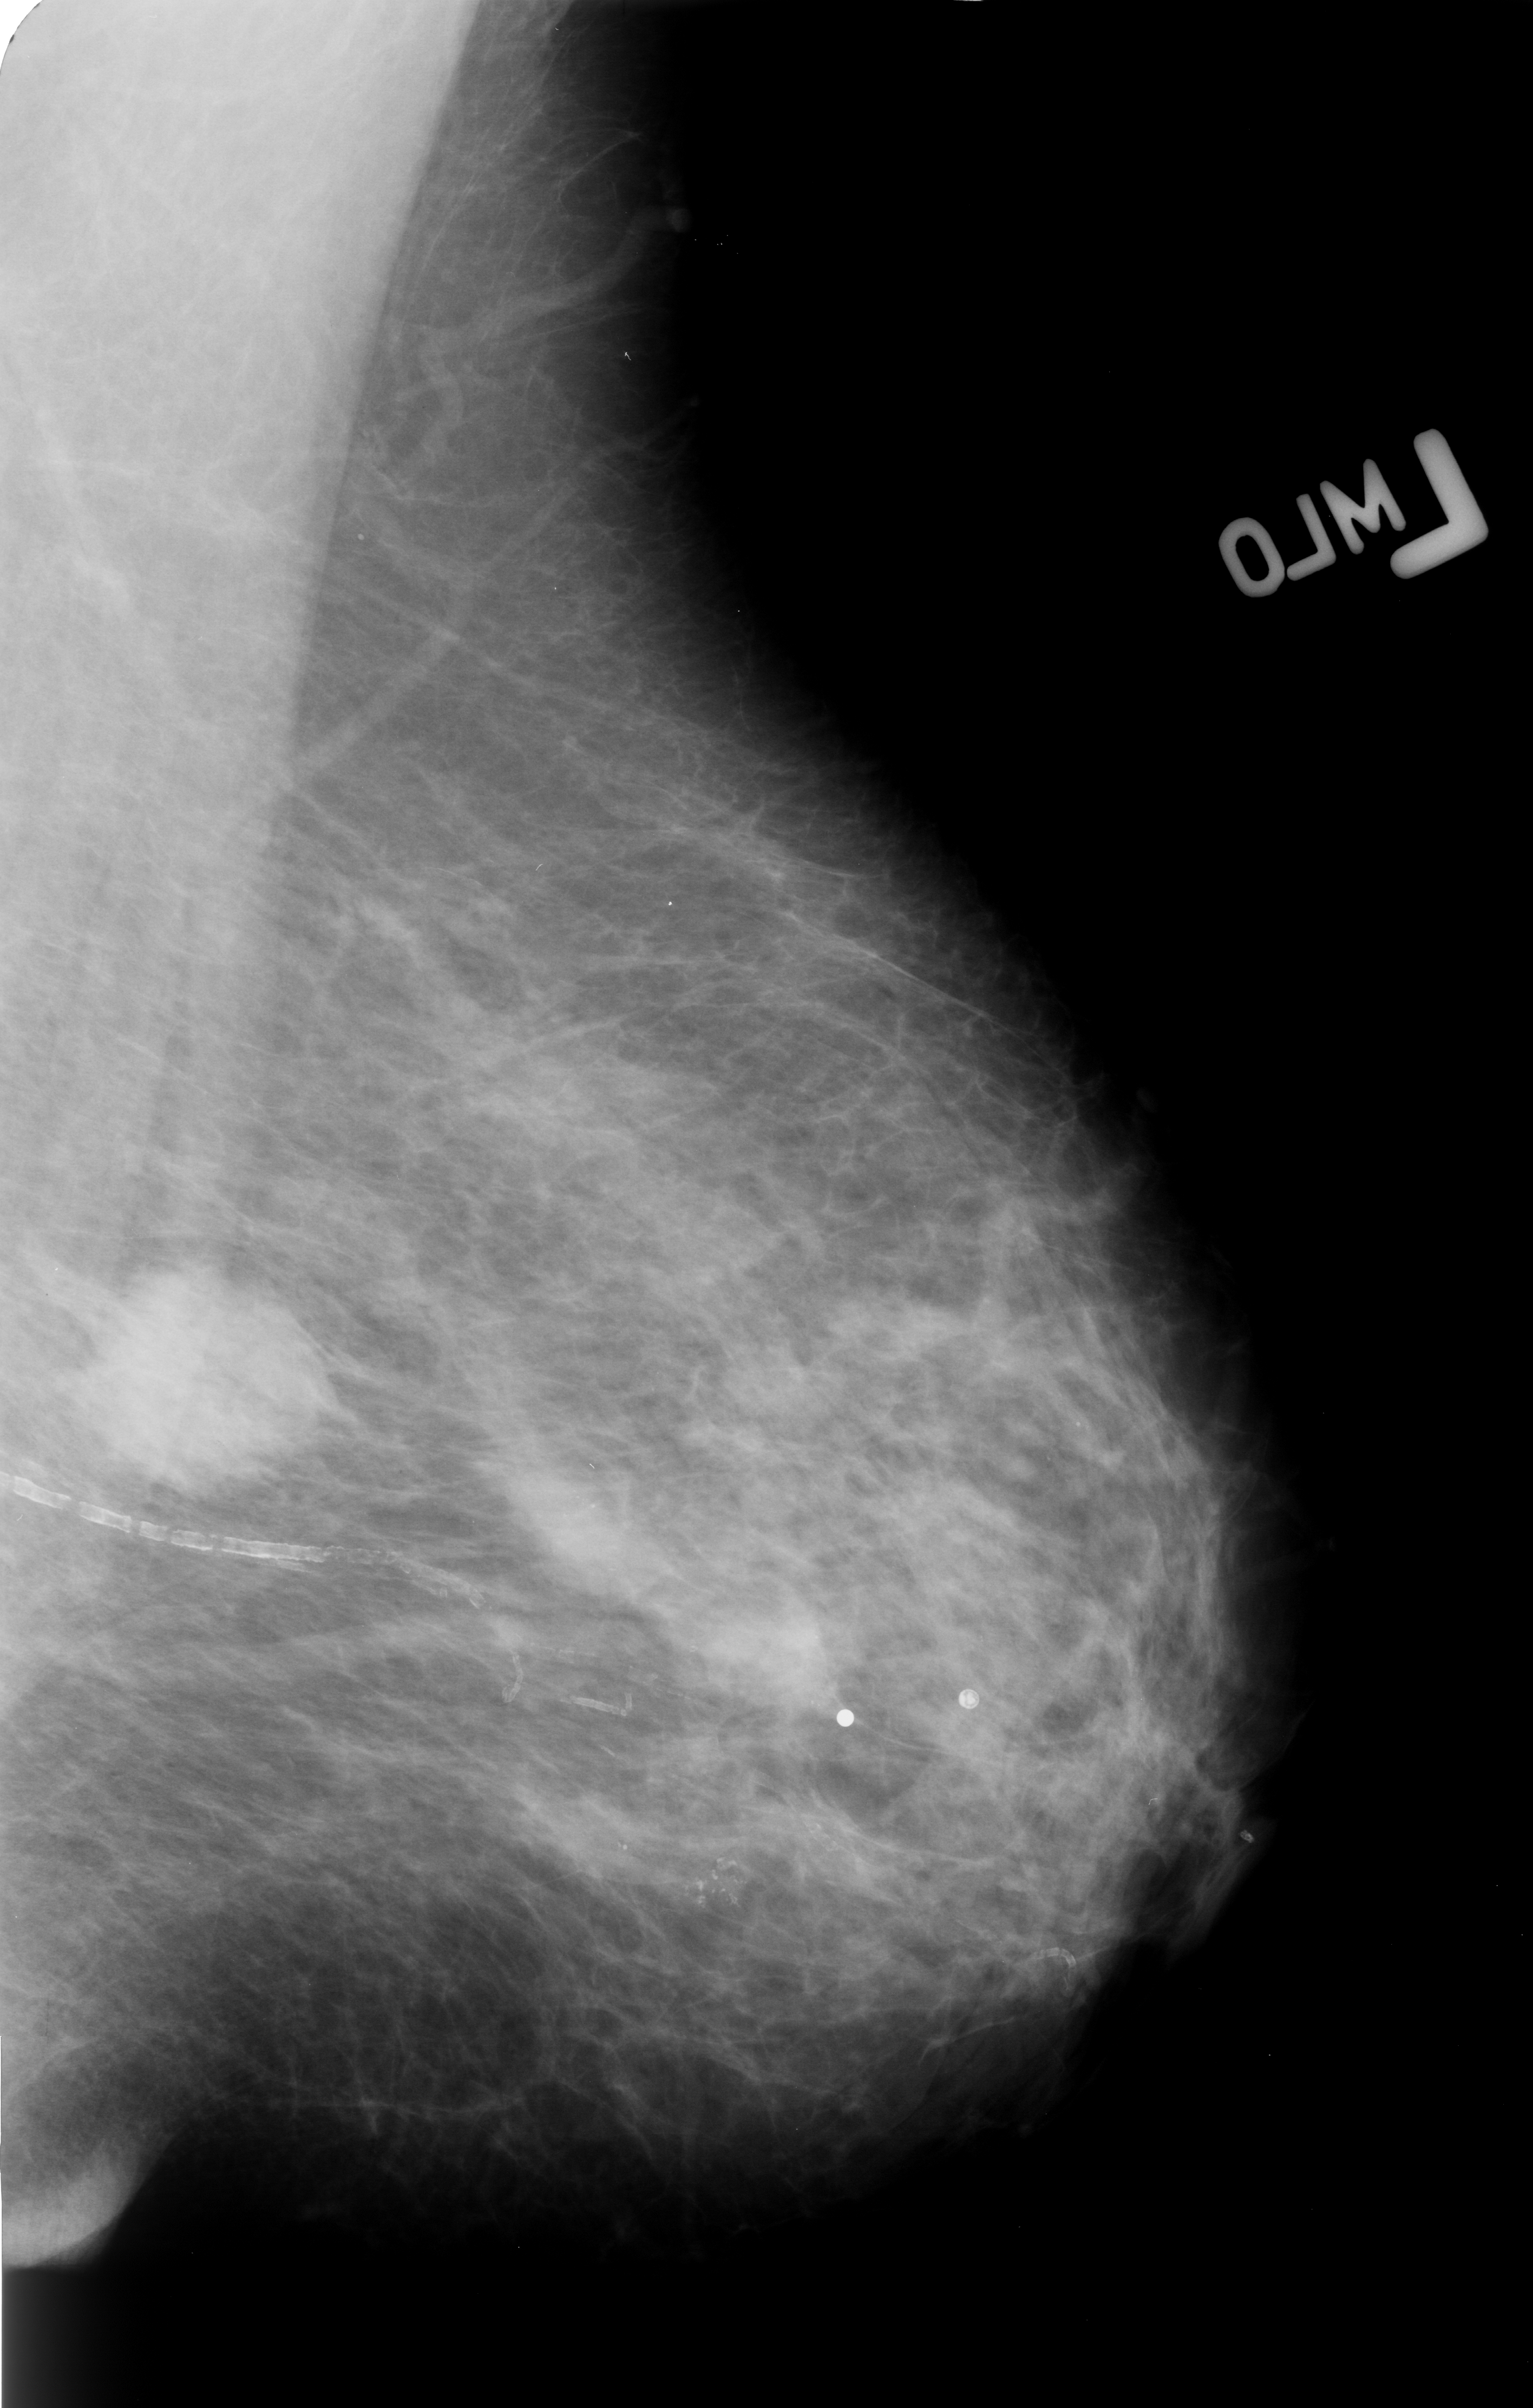
Mammogram (digitized film); left breast; mediolateral oblique (MLO) view; breast composition: scattered fibroglandular densities (BI-RADS density category 2 of 4).
Marked abnormality: calcifications, distribution clustered; BI-RADS assessment category 4; pathology result (as recorded, not read from the image): malignant.